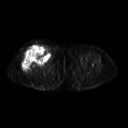
FDG PET of an extremity soft-tissue mass (from a PET/CT study), one axial slice. Position 258 of 311 along the scan axis. 3.27 mm slice thickness. 128 × 128 image matrix, field of view 500 × 500 mm. Patient: female, 57 years. From the clinical record (not read from this slice): histological type: pleiomorphic undifferentiated sarcoma; grade: high; site of the primary tumour: right quadricep.
Annotated regions visible in this slice (expert contour drawn on MRI and transferred to this co-registered scan by the dataset authors):
- tumour plus oedema (research contour): bounding box <22,45,50,72> (left, top, right, bottom; pixels)
- tumour (research contour): <22,45,50,72>